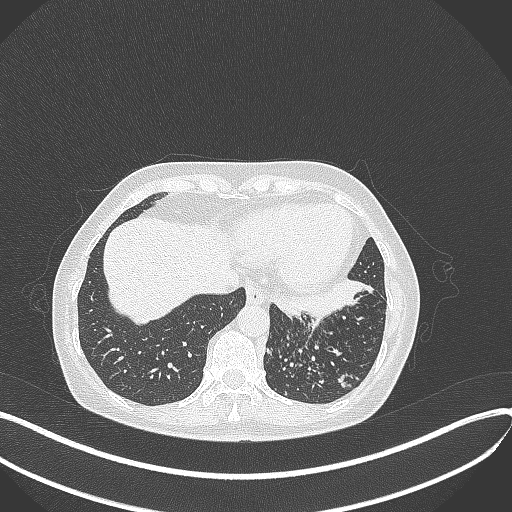
Chest CT, one axial slice; position 102 of 429 along the scan axis; 100 kVp; lung window (W 1500 / L -600 HU); 512 × 512 image matrix, field of view 400 × 400 mm. Female patient, age 63 years. Case-level facts recorded for this patient, not image findings: clinical TNM (as recorded): T1b N0 M0; histopathological grade: G2-3.
Outlined on this slice (rectangle marked by the reading radiologist):
- lung tumour (recorded histology: adenocarcinoma): bounding box (x1, y1, x2, y2) in pixels: (270, 276, 376, 324)